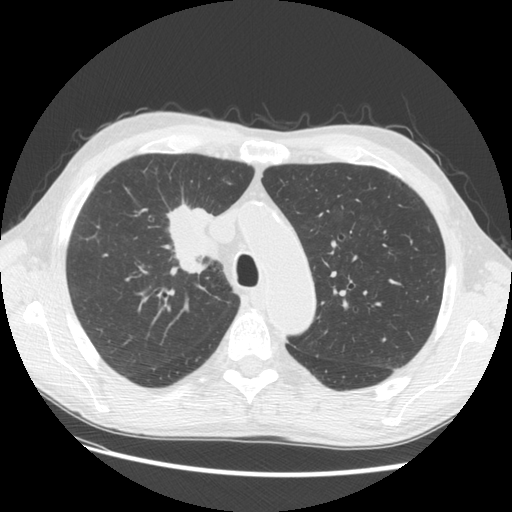
Low-dose screening chest CT, one axial slice. Slice 98 of 133 in the series (ordered by position). Reconstruction kernel STANDARD. 120 kVp. Lung window (W 1500 / L -600 HU). 2.5 mm slice thickness. 512 × 512 image matrix, field of view 360 × 360 mm.
Structures marked on this image (expert manual segmentation):
- lesion 1 (tumor, hilum of right lung): bounding box <166,204,220,274> (left, top, right, bottom; pixels)